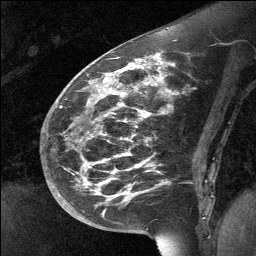
Breast MRI (dynamic contrast-enhanced), one sagittal slice; slice 27 of 64 in the series (ordered by position); dynamic contrast-enhanced study with each time point stored as its own series, time point 2 of 3 at this slice position (early post-contrast, ordered by acquisition time); 1.5 T; TE 4.8 ms, TR 27 ms; 2 mm slice thickness; 256 × 256 image matrix, field of view 200 × 200 mm. Patient: female, 39 years. Case-level facts recorded for this patient, not image findings: setting: breast cancer imaged before/during neoadjuvant chemotherapy; receptor status: HER2-positive.
Annotated regions visible in this slice (semi-automatically segmented with operator editing):
- analysis volume of interest (the breast-tissue region the enhancement analysis was run in; not a lesion): bounding box <70,69,173,224> (left, top, right, bottom; pixels)
- tumour enhancement mask (voxels above the 90 % enhancement threshold inside the analysis volume of interest): <99,69,125,185>